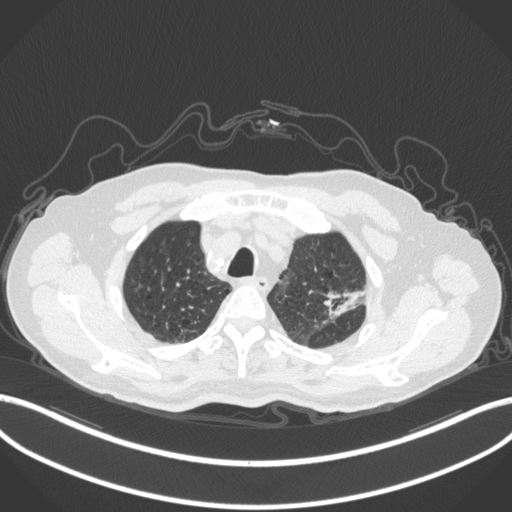
Chest CT, one axial slice. Position 252 of 331 along the scan axis. Lung window (W 1500 / L -600 HU). 1 mm slice thickness. 512 × 512 image matrix. Patient: male, 79 years. Case-level facts recorded for this patient, not image findings: clinical TNM (as recorded): T2a N1 M1.
Annotated regions visible in this slice (bounding box drawn by a radiologist):
- lung tumour (recorded histology: adenocarcinoma): bounding box [x1, y1, x2, y2] px = [323, 283, 376, 319]